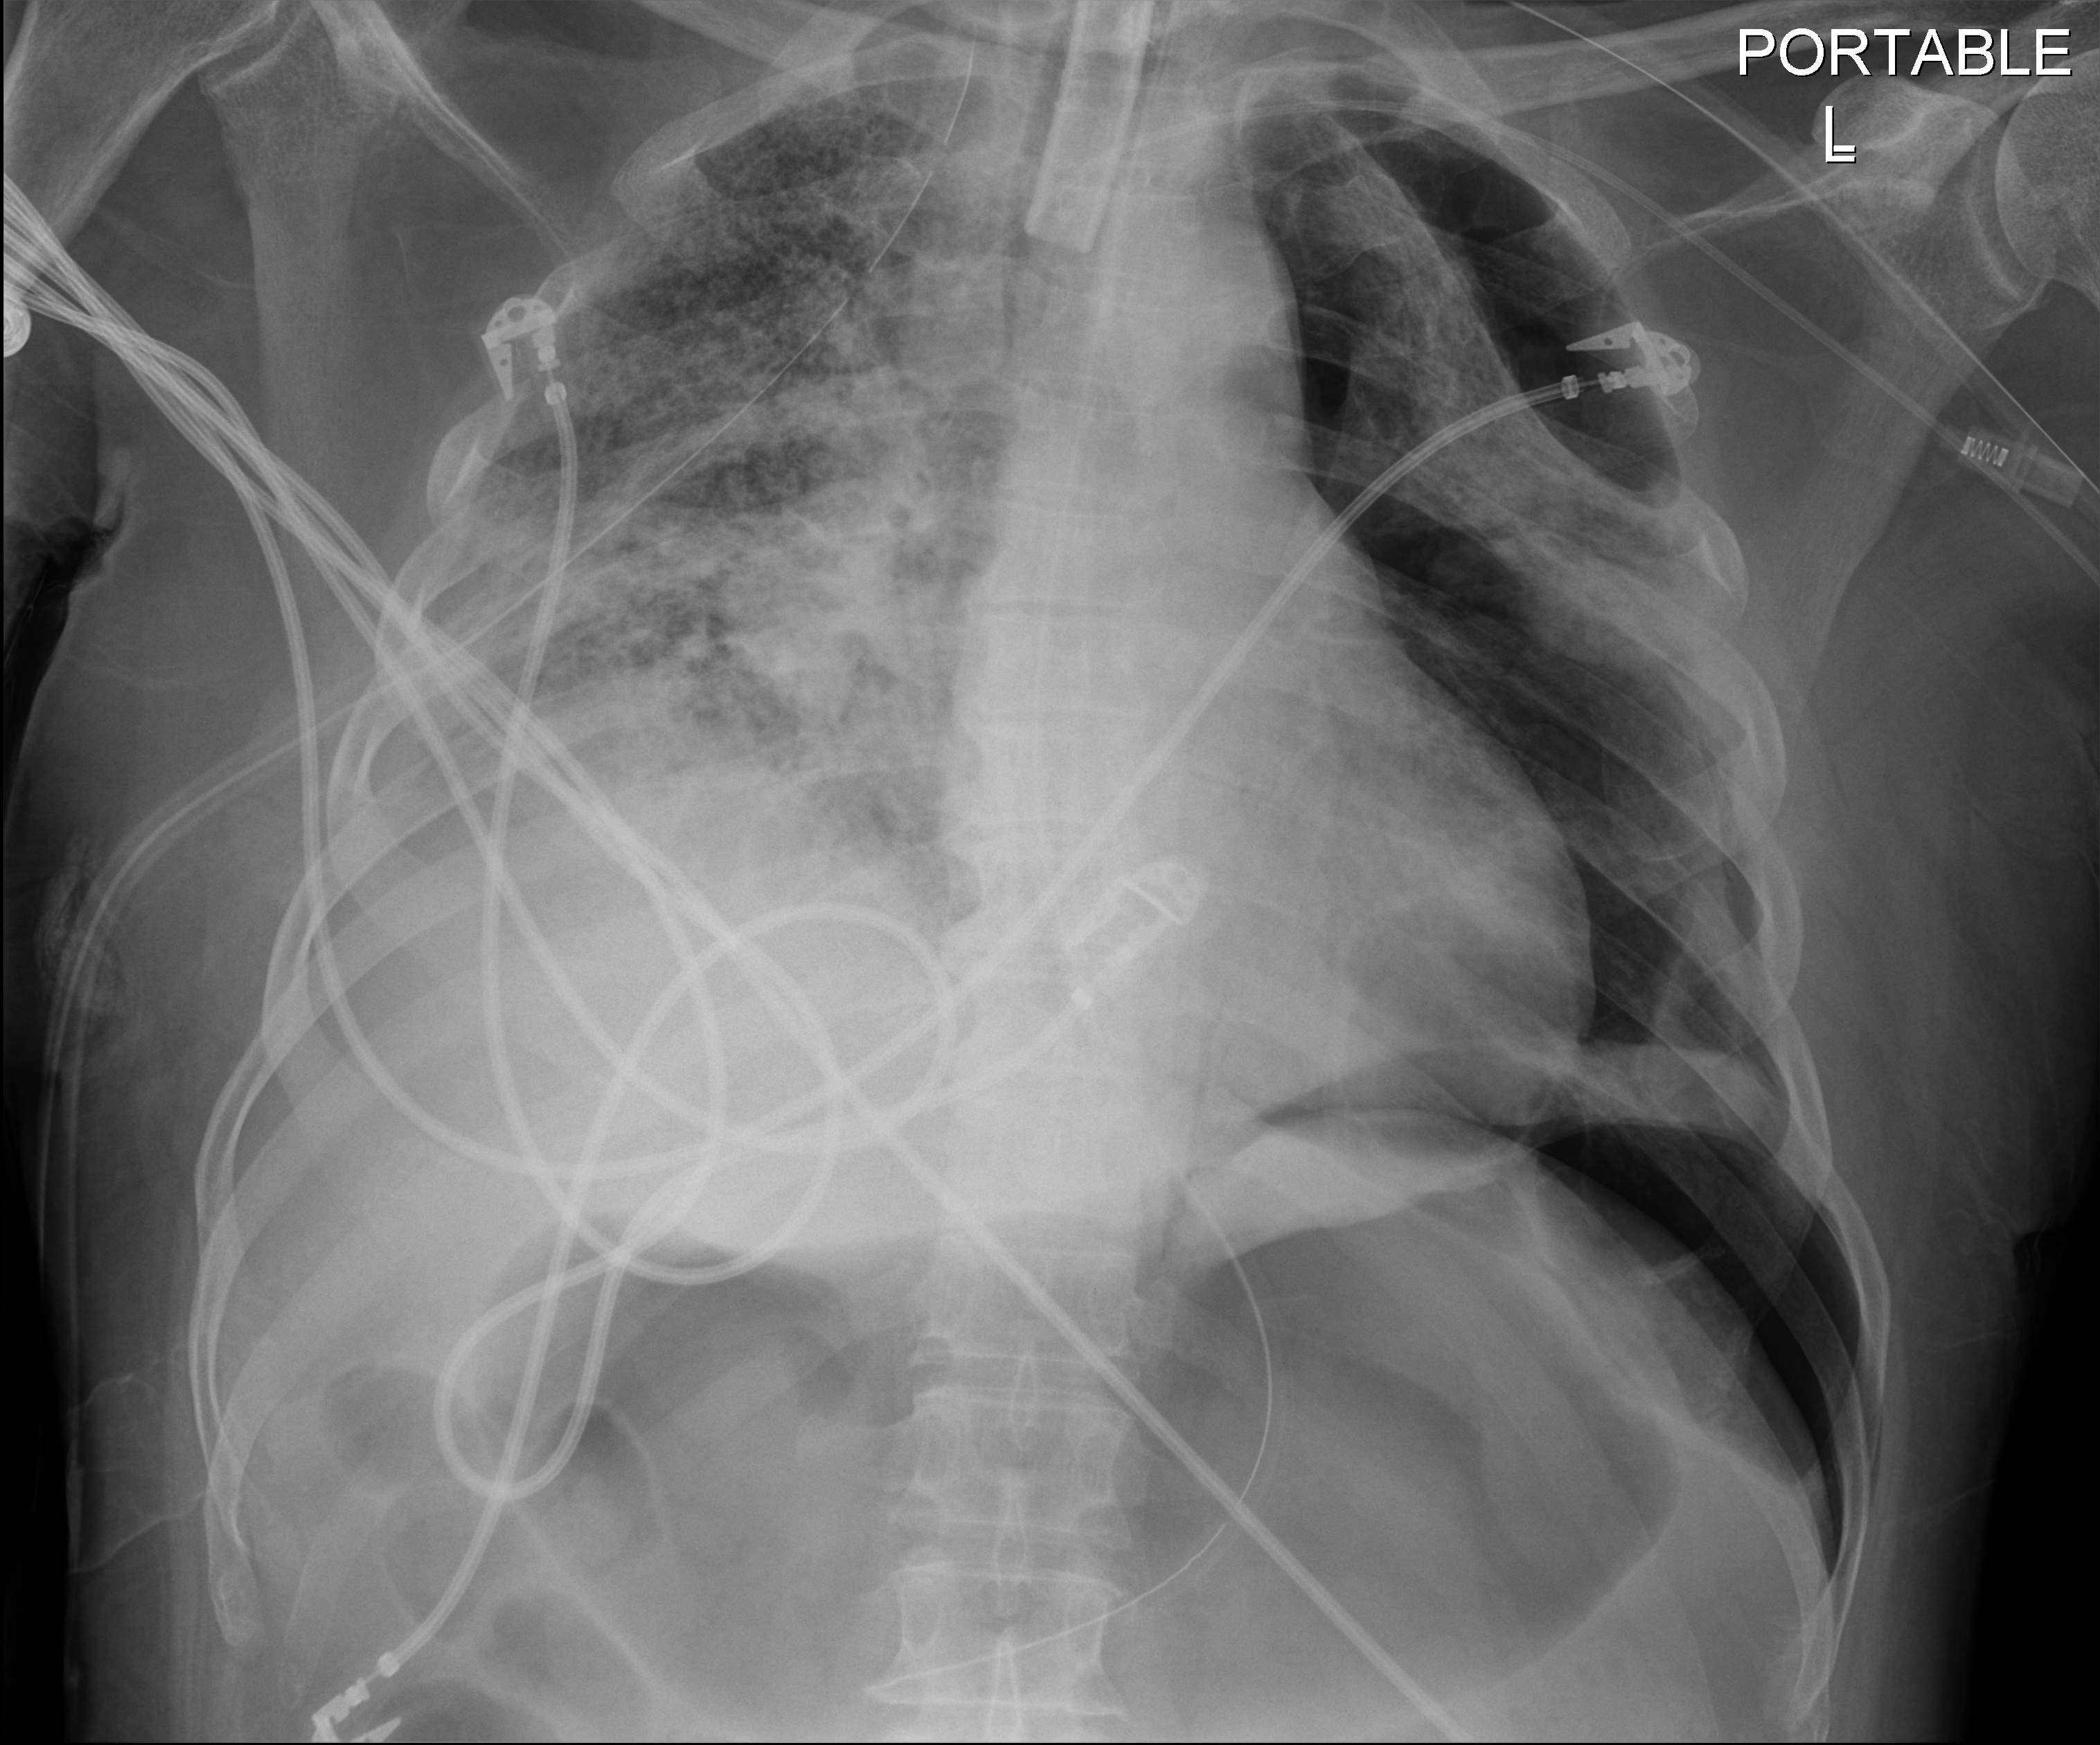
Portable chest radiograph; anteroposterior (AP) projection. Patient hospitalised with COVID-19; male, aged 18–59 years.
Admission-level facts for this patient (not findings on this image; timing relative to this image not recorded):
- other chronic lung disease (admission record): no
- mechanically ventilated during this hospital stay: yes
- admitted to intensive care during this hospital stay: yes